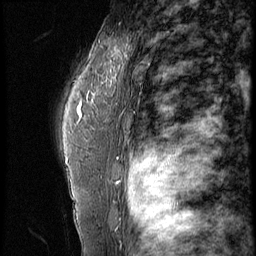
Breast MRI (dynamic contrast-enhanced), one sagittal slice. 4 images stored at this slice position (order not interpretable as contrast timing). 1.5 T. TE 4.2 ms, TR 9 ms. 2.5 mm slice thickness. 256 × 256 image matrix. Patient: female, 44 years. From the clinical record (not read from this slice): setting: breast cancer imaged before/during neoadjuvant chemotherapy; receptor status: triple-negative.
Structures marked on this image (semi-automatic segmentation, software-assisted and operator-edited):
- analysis volume of interest (the breast-tissue region the enhancement analysis was run in; not a lesion): bounding box (x1, y1, x2, y2) in pixels: (87, 28, 132, 99)
- tumour enhancement mask (voxels above the 140 % enhancement threshold inside the analysis volume of interest): (117, 48, 121, 55)